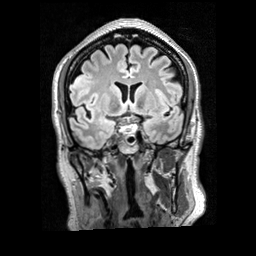
Brain MRI from a brain-tumour surgery series, one coronal slice; slice 118 of 200 in the series (ordered by position); T2 FLAIR; 256 × 256 image matrix. Case-level facts recorded for this patient, not image findings: histopathology: Glioblastoma; WHO grade: 4; IDH mutation: no.
Outlined on this slice (expert manual segmentation):
- tumour: bounding box <69,72,92,89> (left, top, right, bottom; pixels)